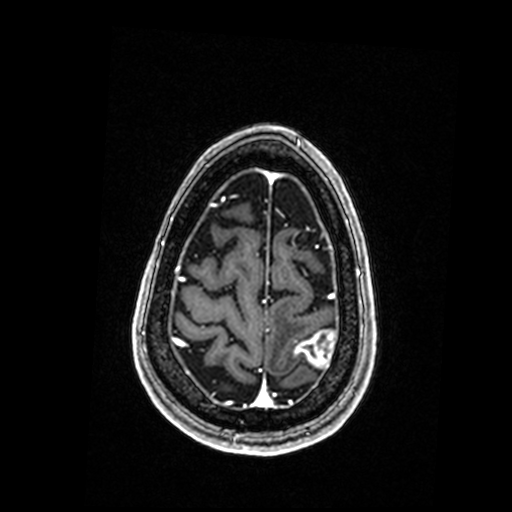
Brain MRI from a brain-tumour surgery series, one axial slice; position 41 of 192 along the scan axis; T1-weighted post-contrast; 0.98 mm slice thickness; 512 × 512 image matrix, field of view 250 × 250 mm. From the clinical record (not read from this slice): histopathology: Metastastic Carcinoma, Poorly Differentiated; tumour location: Left Parietal.
Structures marked on this image (expert manual segmentation):
- tumour: bounding box [x1, y1, x2, y2] px = [295, 331, 334, 368]